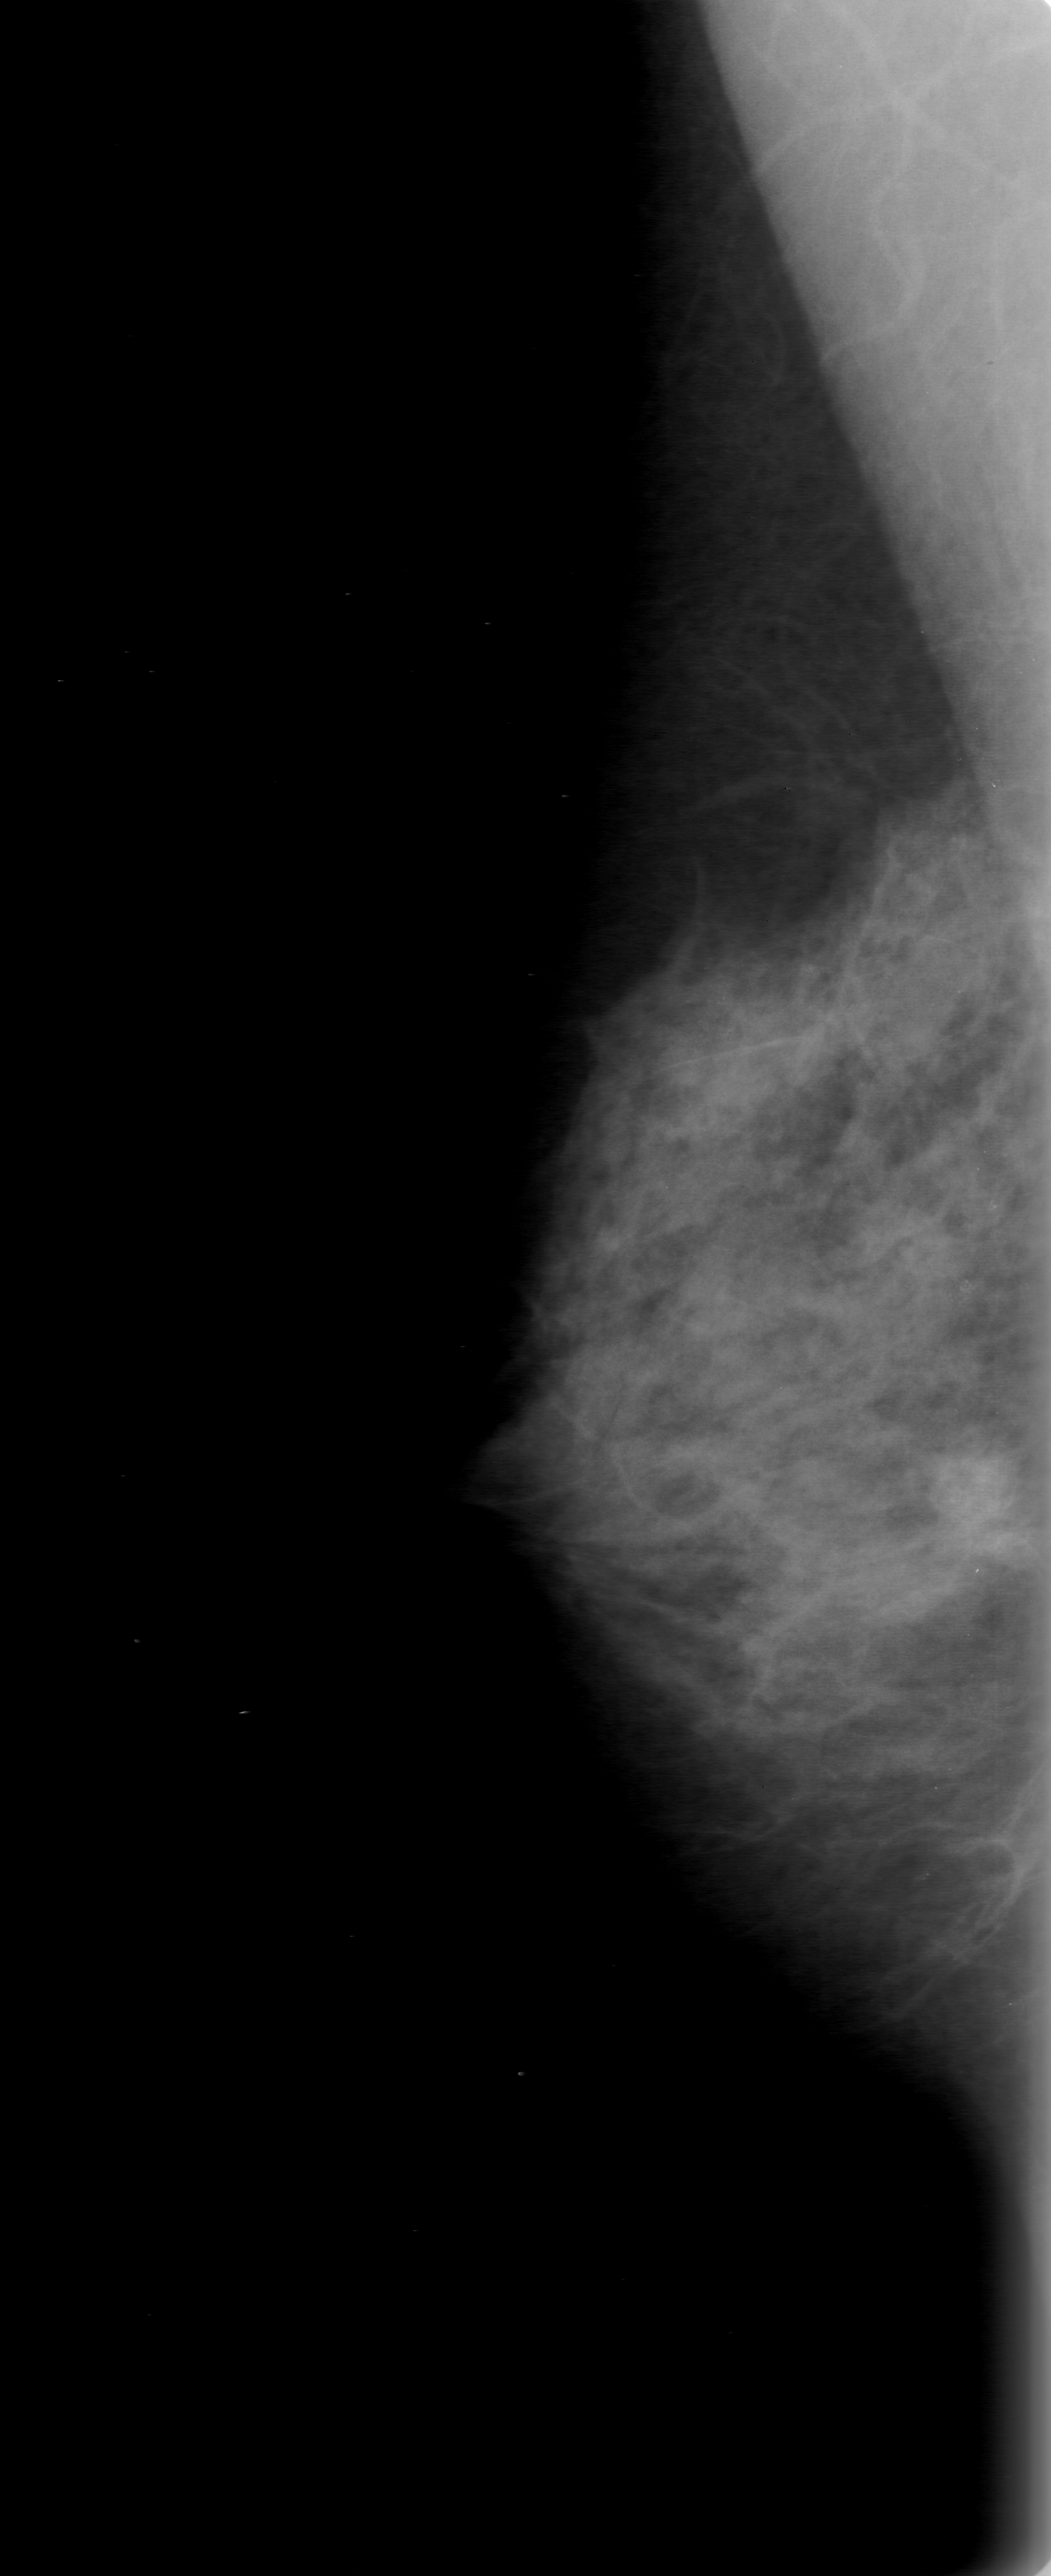
Scanned film-screen mammogram, right breast, MLO view, BI-RADS breast density category 3 (scale 1–4).
Marked abnormality: mass, shape irregular, margins ill defined; BI-RADS assessment category 0; subtlety rating 4 on a 1 (subtle) to 5 (obvious) scale; pathology result (as recorded, not read from the image): malignant.